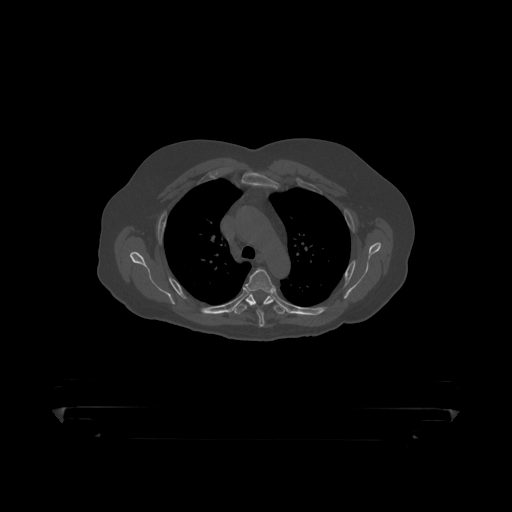
CT including the spine, one axial slice. Position 331 of 390 along the scan axis. Reconstruction kernel STANDARD. 120 kVp. Bone window (W 1800 / L 400 HU). 1.25 mm slice thickness. 512 × 512 image matrix, field of view 650 × 650 mm. Male patient, age 60 years. From the clinical record (not read from this slice): primary cancer: prostate.
Annotated regions visible in this slice (semi-automatically segmented with operator editing):
- T4 vertebra: box from (x=246, y=269) to (x=276, y=319) px
- T5 vertebra: (x=233, y=293)–(x=287, y=315)